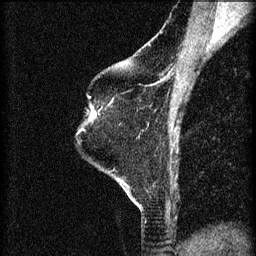
Breast MRI (dynamic contrast-enhanced), one sagittal slice. Position 47 of 60 along the scan axis. 3 images stored at this slice position (order not interpretable as contrast timing). 1.5 T. TE 4.2 ms, TR 8.2 ms. 2 mm slice thickness. 256 × 256 image matrix, field of view 180 × 180 mm. Female patient, age 60 years.
Outlined on this slice (semi-automatically segmented with operator editing):
- analysis volume of interest (the breast-tissue region the enhancement analysis was run in; not a lesion): box from (x=79, y=98) to (x=96, y=131) px
- tumour enhancement mask (voxels above the 70 % enhancement threshold inside the analysis volume of interest): (x=90, y=110)–(x=96, y=121)